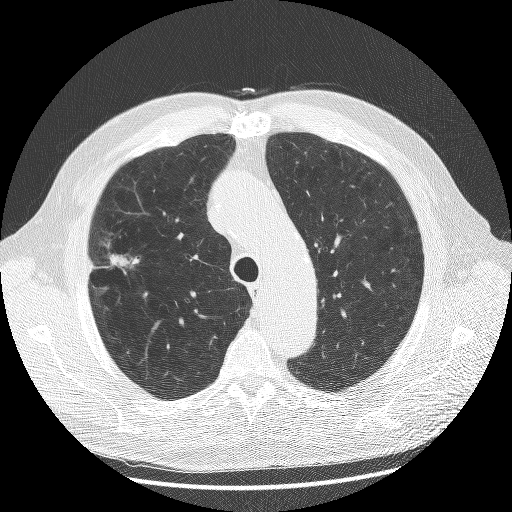
Low-dose screening chest CT, axial slice, baseline screening round, lung window (W 1500 / L -600 HU), 2.5 mm slice thickness, slice 37 of 175 in the series. Male, age 70 years at enrolment. Current smoker at enrolment.
- Lesion marked by an expert reader, bounding box [x1, y1, x2, y2] px = [79, 231, 146, 305].
- The screening reader recorded 2 non-calcified nodules or masses ≥4 mm on this exam (left upper lobe, right upper lobe); which of them this box marks is not recorded.
- Later outcome: lung cancer diagnosed 23 days after this screen — non-small cell carcinoma, right upper lobe, poorly differentiated (G3), stage IA (AJCC 6th edition), 20 mm at pathology.